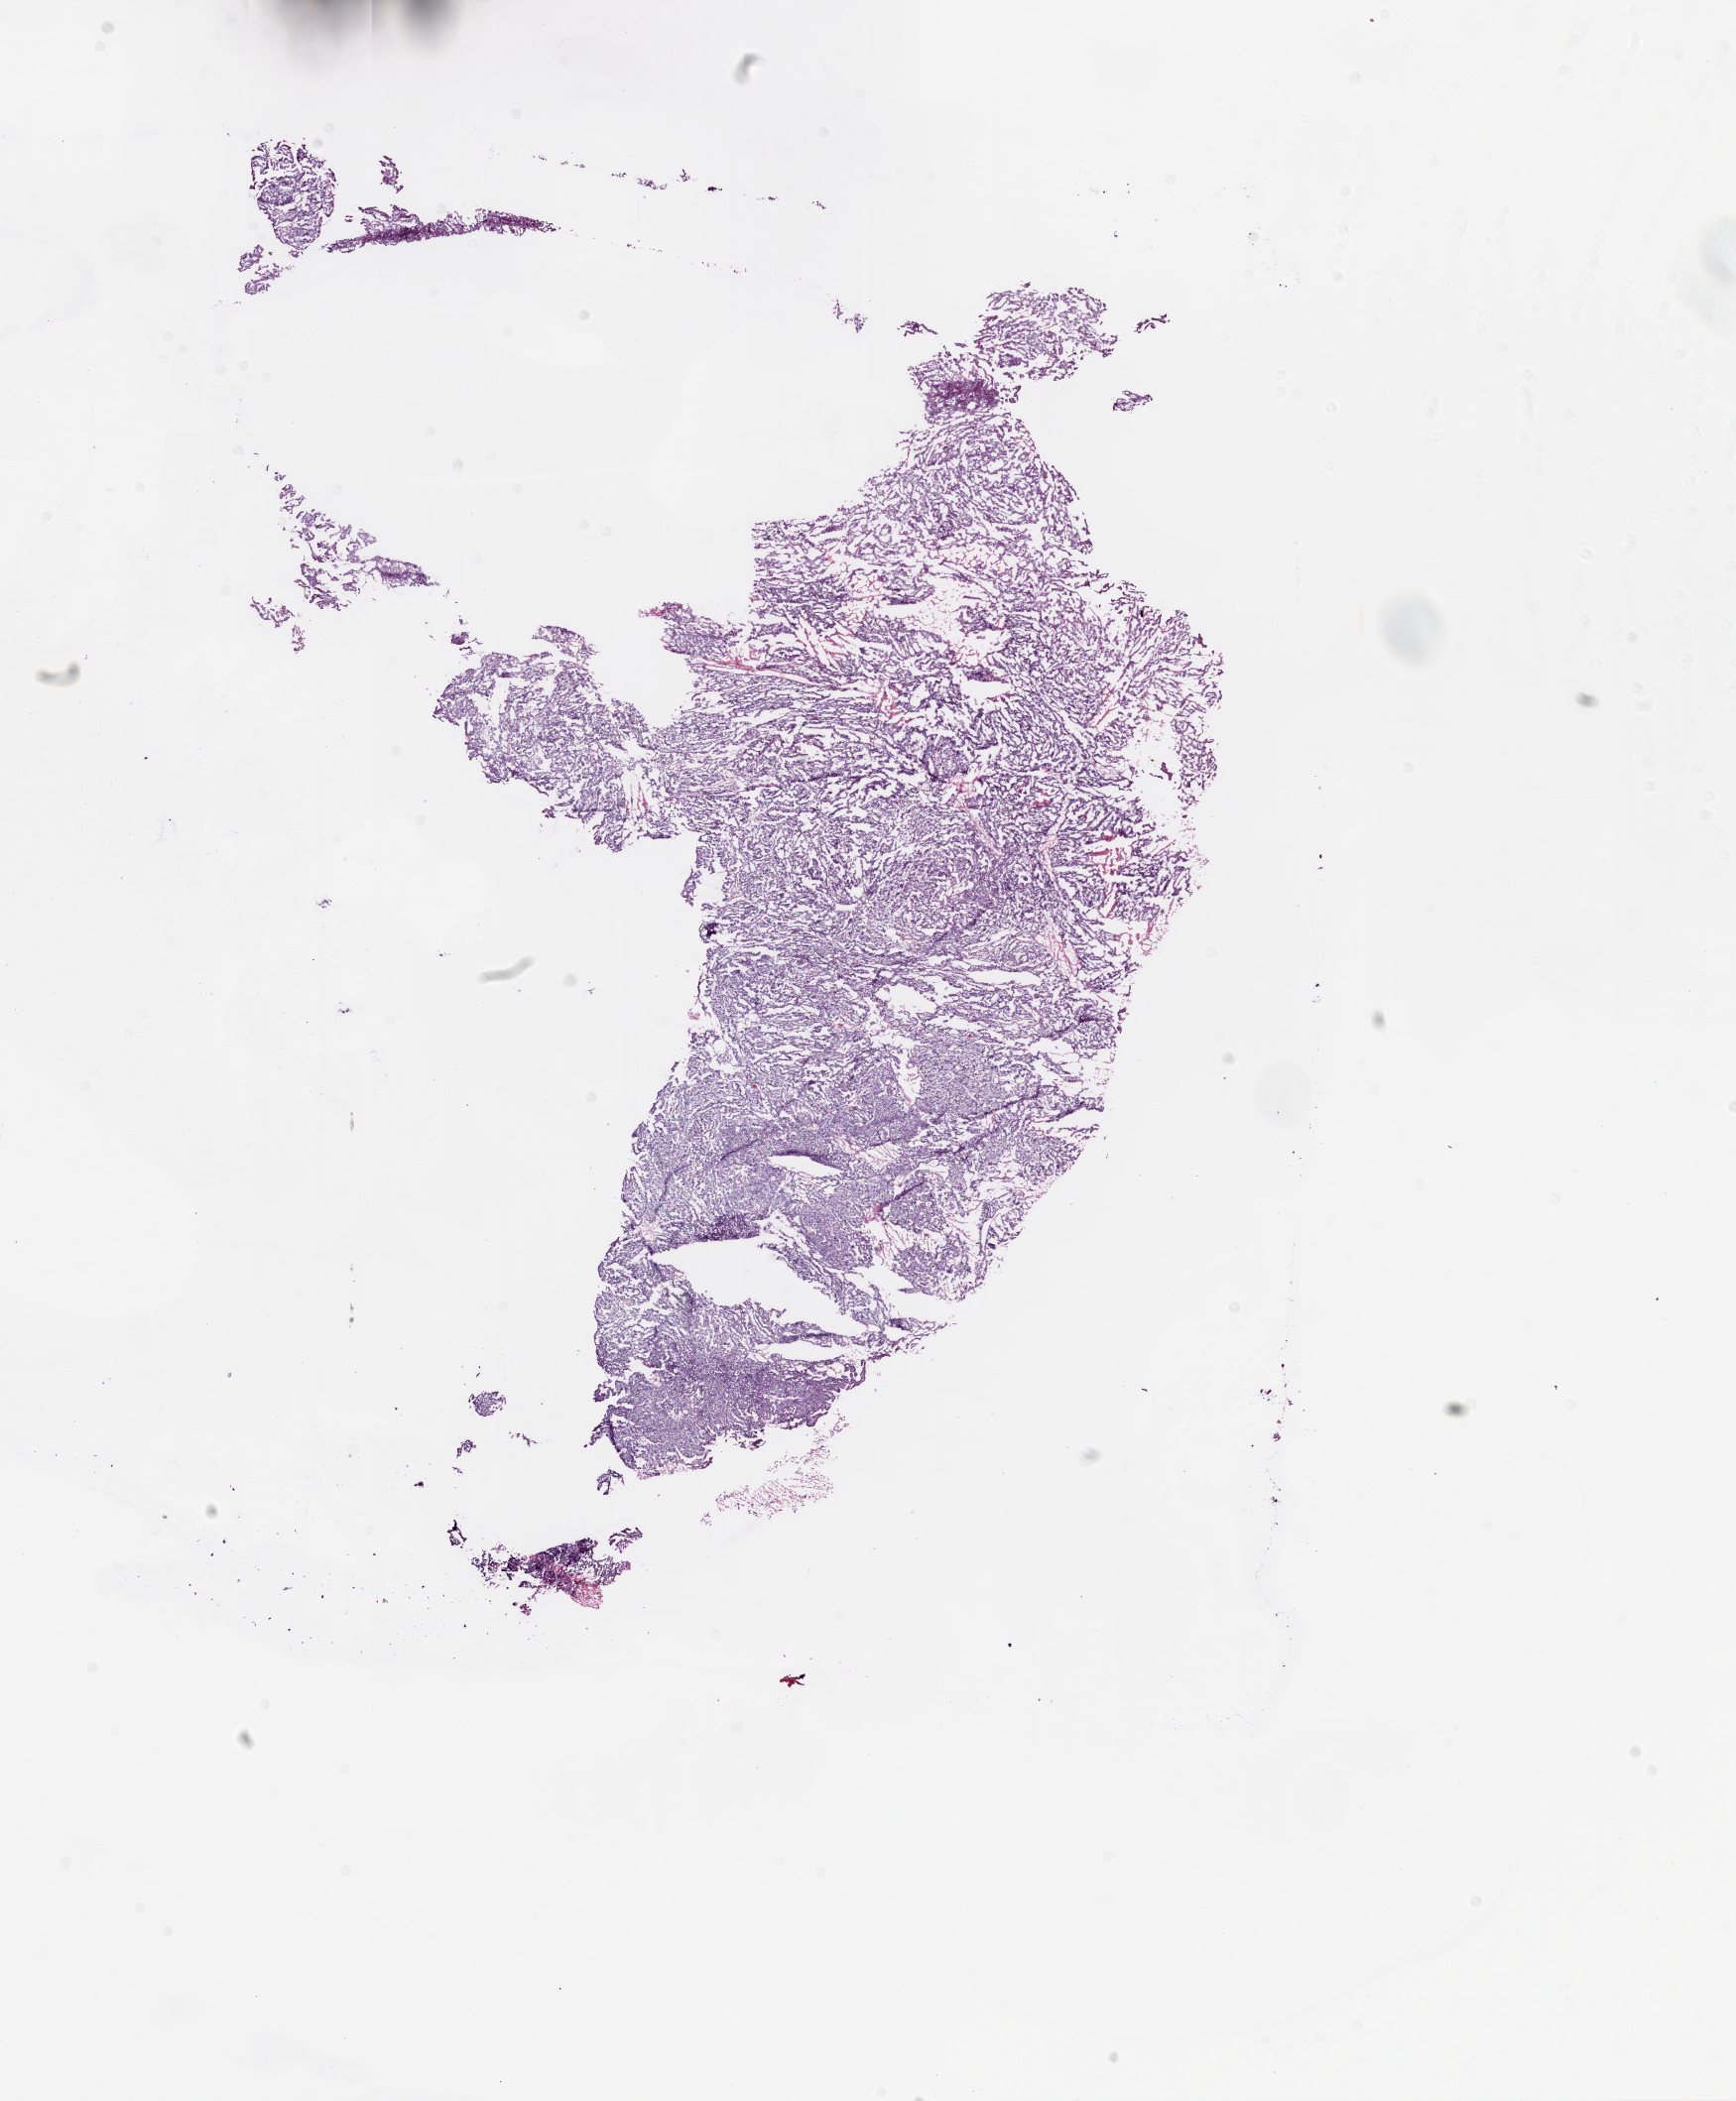
Whole-slide histology image, Hematoxylin and eosin (H&E) stained — a low-resolution overview of the entire scanned area, about 14.0 x 17.0 mm (acquisition: 20x scan); frozen section from the bottom of the tissue portion; primary tumour sample from the ovary. Female, age 58 years at initial diagnosis. Histologic grade: G3 (poorly differentiated). Composition of this section per pathologist review: tumour cells 98%, tumour nuclei 99%, normal cells 0%, stromal cells 1%, necrosis 1%.
* FIGO stage: IIIC
* laterality: bilateral
* pathologic diagnosis: Serous cystadenocarcinoma, NOS